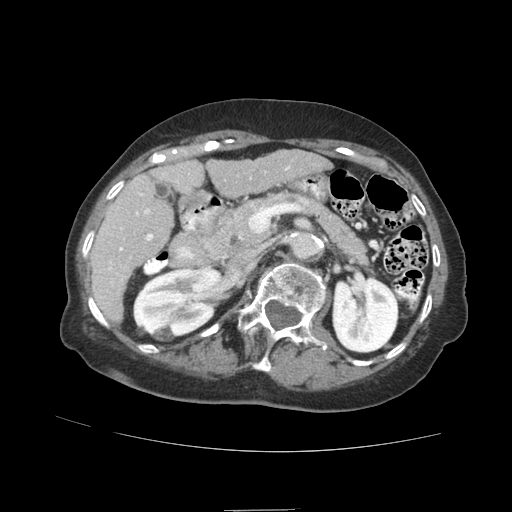
Contrast-enhanced abdominal CT (liver protocol), one axial slice; soft-tissue window (W 400 / L 40 HU); 2.5 mm slice thickness; 512 × 512 image matrix, field of view 360 × 360 mm. Case-level facts recorded for this patient, not image findings: diagnosis: hepatocellular carcinoma (patient treated with transarterial chemoembolisation; whether this scan precedes or follows treatment is not stated here); TNM stage (as recorded): Stage-II; Child-Pugh class: A; tumour differentiation: moderately differentiated; tumour nodularity: multinodular.
Annotated regions visible in this slice (semi-automatic segmentation, software-assisted and operator-edited):
- liver parenchyma outside the tumour (the mass and vessels are separate outlines, so this box may not span the whole liver): bounding box (x1, y1, x2, y2) in pixels: (90, 150, 330, 320)
- liver vessels: (109, 166, 290, 284)